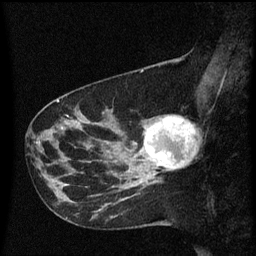
Breast MRI (dynamic contrast-enhanced), one sagittal slice. Dynamic contrast-enhanced series, image 2 of 3 at this slice position (ordered by acquisition). 1.5 T. TE 4.2 ms, TR 8.4 ms. 2 mm slice thickness. 256 × 256 image matrix, field of view 200 × 200 mm. Patient: female, 41 years. Case-level facts recorded for this patient, not image findings: setting: breast cancer imaged before/during neoadjuvant chemotherapy; receptor status: triple-negative.
Outlined on this slice (semi-automatic segmentation, software-assisted and operator-edited):
- analysis volume of interest (the breast-tissue region the enhancement analysis was run in; not a lesion): bounding box (x1, y1, x2, y2) in pixels: (138, 116, 196, 177)
- tumour enhancement mask (voxels above the 70 % enhancement threshold inside the analysis volume of interest): (144, 116, 194, 171)